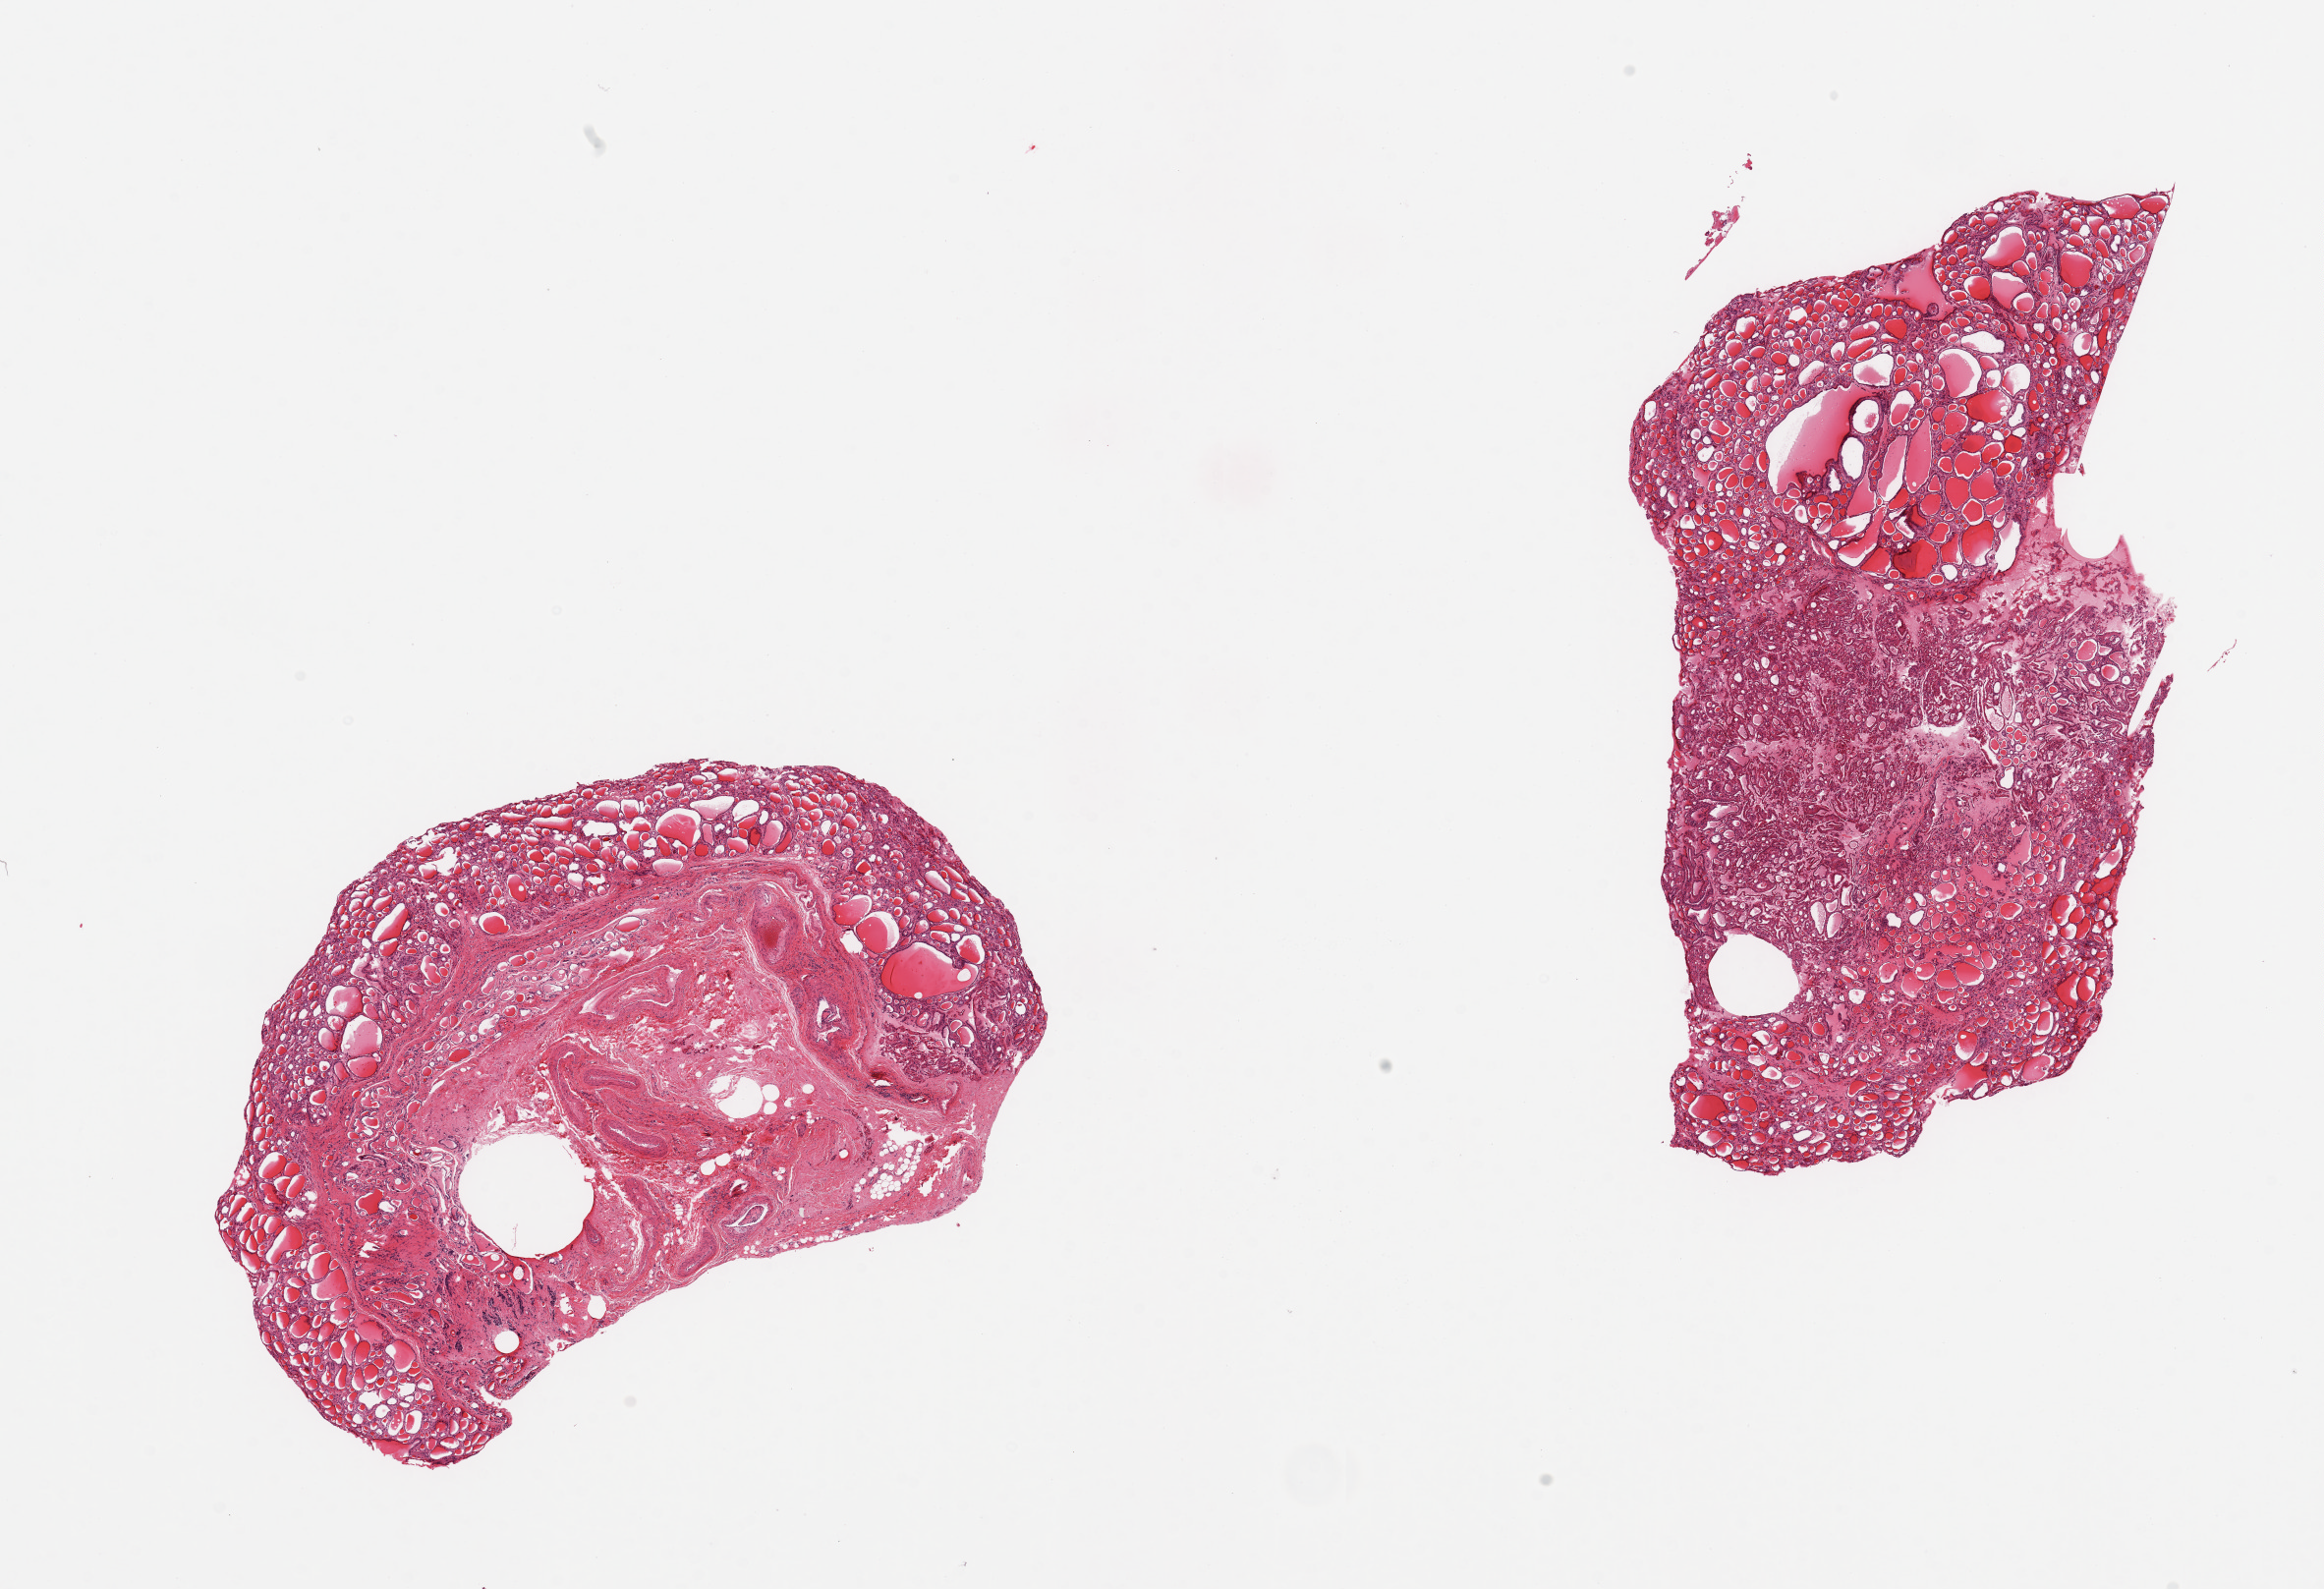
Digitized hematoxylin and eosin (H&E)-stained section, a low-resolution overview of the entire scanned area, about 18.7 x 12.8 mm, PAXgene-fixed, paraffin-embedded tissue, section of thyroid (target tissue), donor tissue sample. Female donor.
Pathologist's review note for this sample: 2 pieces: 1 with 40% oncocytic change, other with 5% and with 50% large blood vessels and stroma.